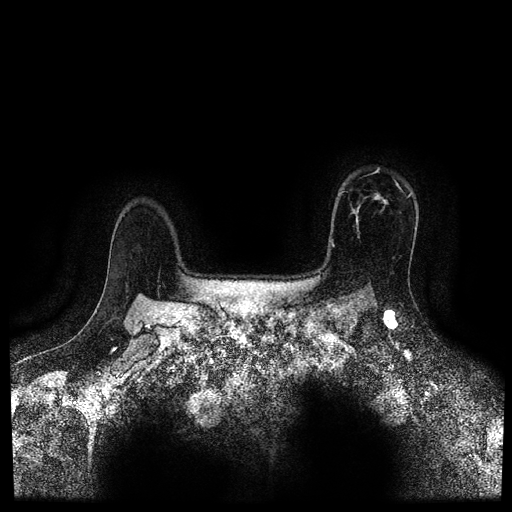
Breast MRI (dynamic contrast-enhanced, multi-phase), one axial slice. Dynamic contrast-enhanced series, time point 2 of 5 at this slice position (early post-contrast). 1.5 T. TE 2.7 ms, TR 5.4 ms. 2 mm slice thickness. 512 × 512 image matrix, field of view 340 × 340 mm. Female patient, age 50 years.
Annotated regions visible in this slice (semi-automatic segmentation, software-assisted and operator-edited):
- breast lesion (labelled 'tumour' in the annotation; benign lesions carry a separate 'benign' label): bounding box [x1, y1, x2, y2] px = [372, 190, 390, 209]